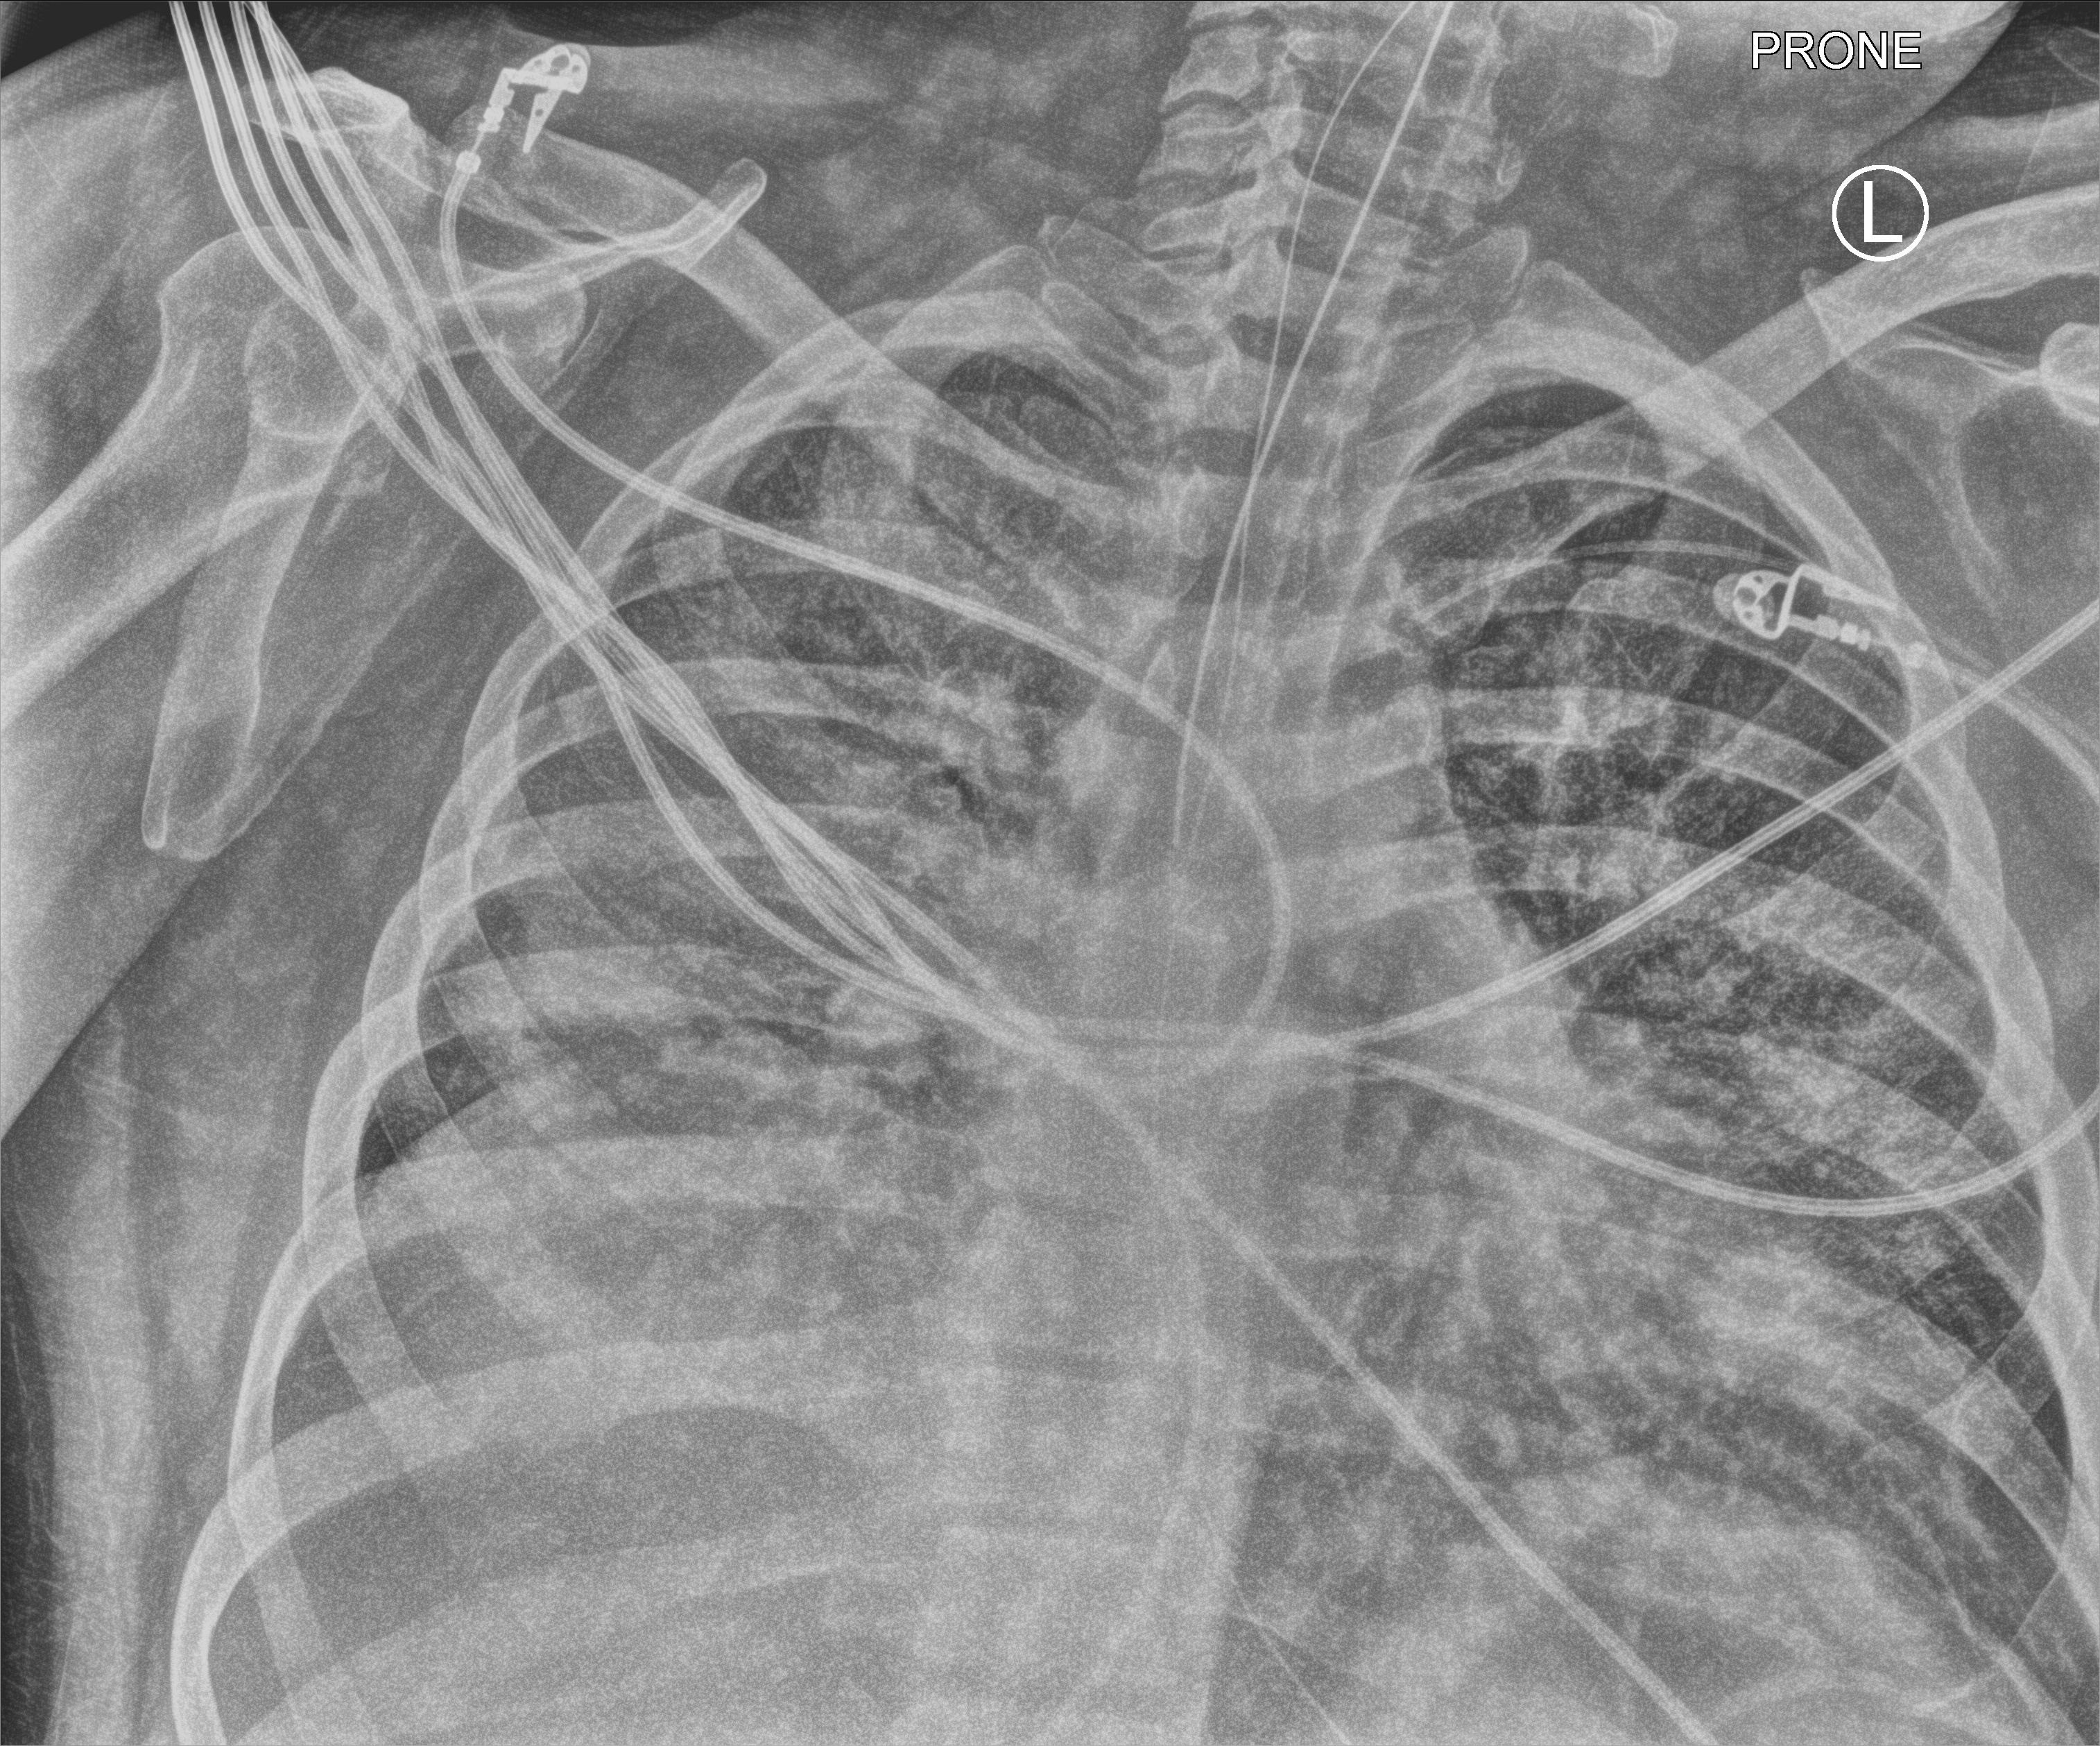
Bedside chest radiograph (computed radiography); anteroposterior (AP) projection. Male patient hospitalised with COVID-19, age 18–59 years.
Admission-level facts for this patient (not findings on this image; timing relative to this image not recorded):
- mechanically ventilated during this hospital stay: yes